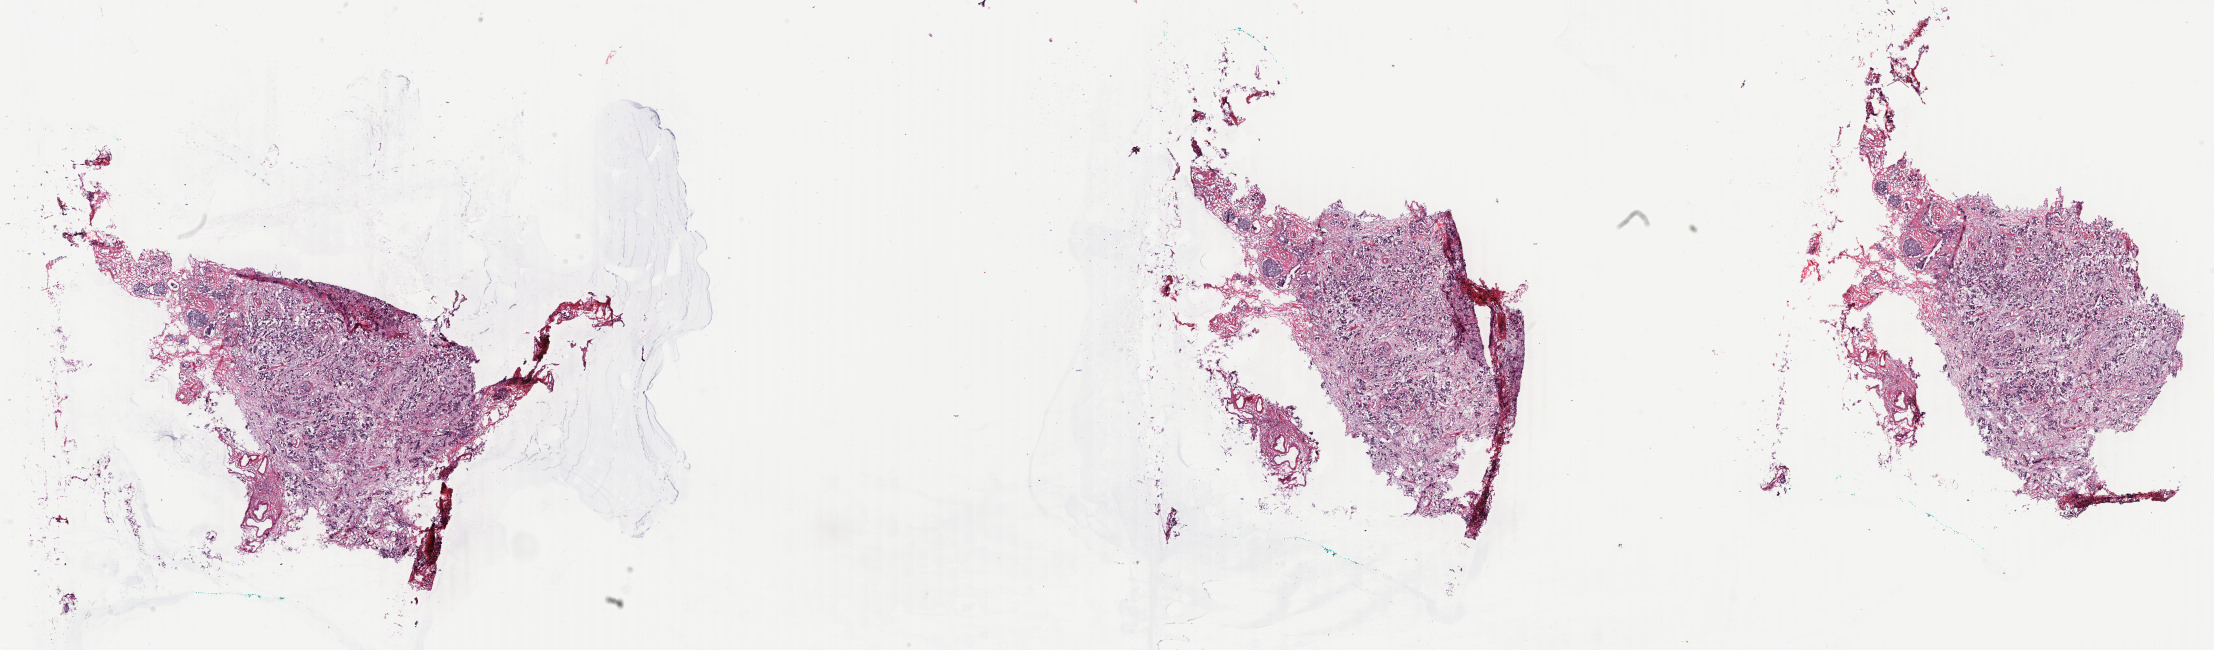
H&E whole-slide image — low-resolution overview of the scanned area, about 35.2 x 10.3 mm (slide scanned at 40x), frozen section, primary tumour sample from the breast. Female patient; age at initial diagnosis 41 years. Pathologist review of this section (percent, as recorded): tumour cells 50%, tumour nuclei 65%, normal cells 10%, stromal cells 39%, necrosis 1%. Infiltration values recorded for this section: lymphocyte infiltration 5%, monocyte infiltration 0%, neutrophil infiltration 0%.
* diagnosis: Infiltrating duct carcinoma, NOS
* lymph nodes positive (case pathology): 0 of 2 examined
* TNM: T1c N0 (i-) M0
* AJCC pathologic stage: I (6th edition)